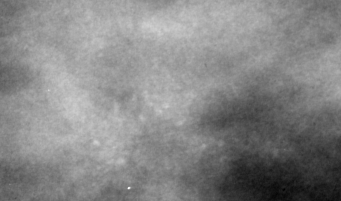
Region of interest cut from a scanned film mammogram (one marked finding); left breast; CC view; BI-RADS breast density category 4 (scale 1–4).
- Calcifications, morphology pleomorphic, distribution clustered; BI-RADS assessment category 4; subtlety rating 1 on a 1 (subtle) to 5 (obvious) scale; pathology (as recorded): malignant.